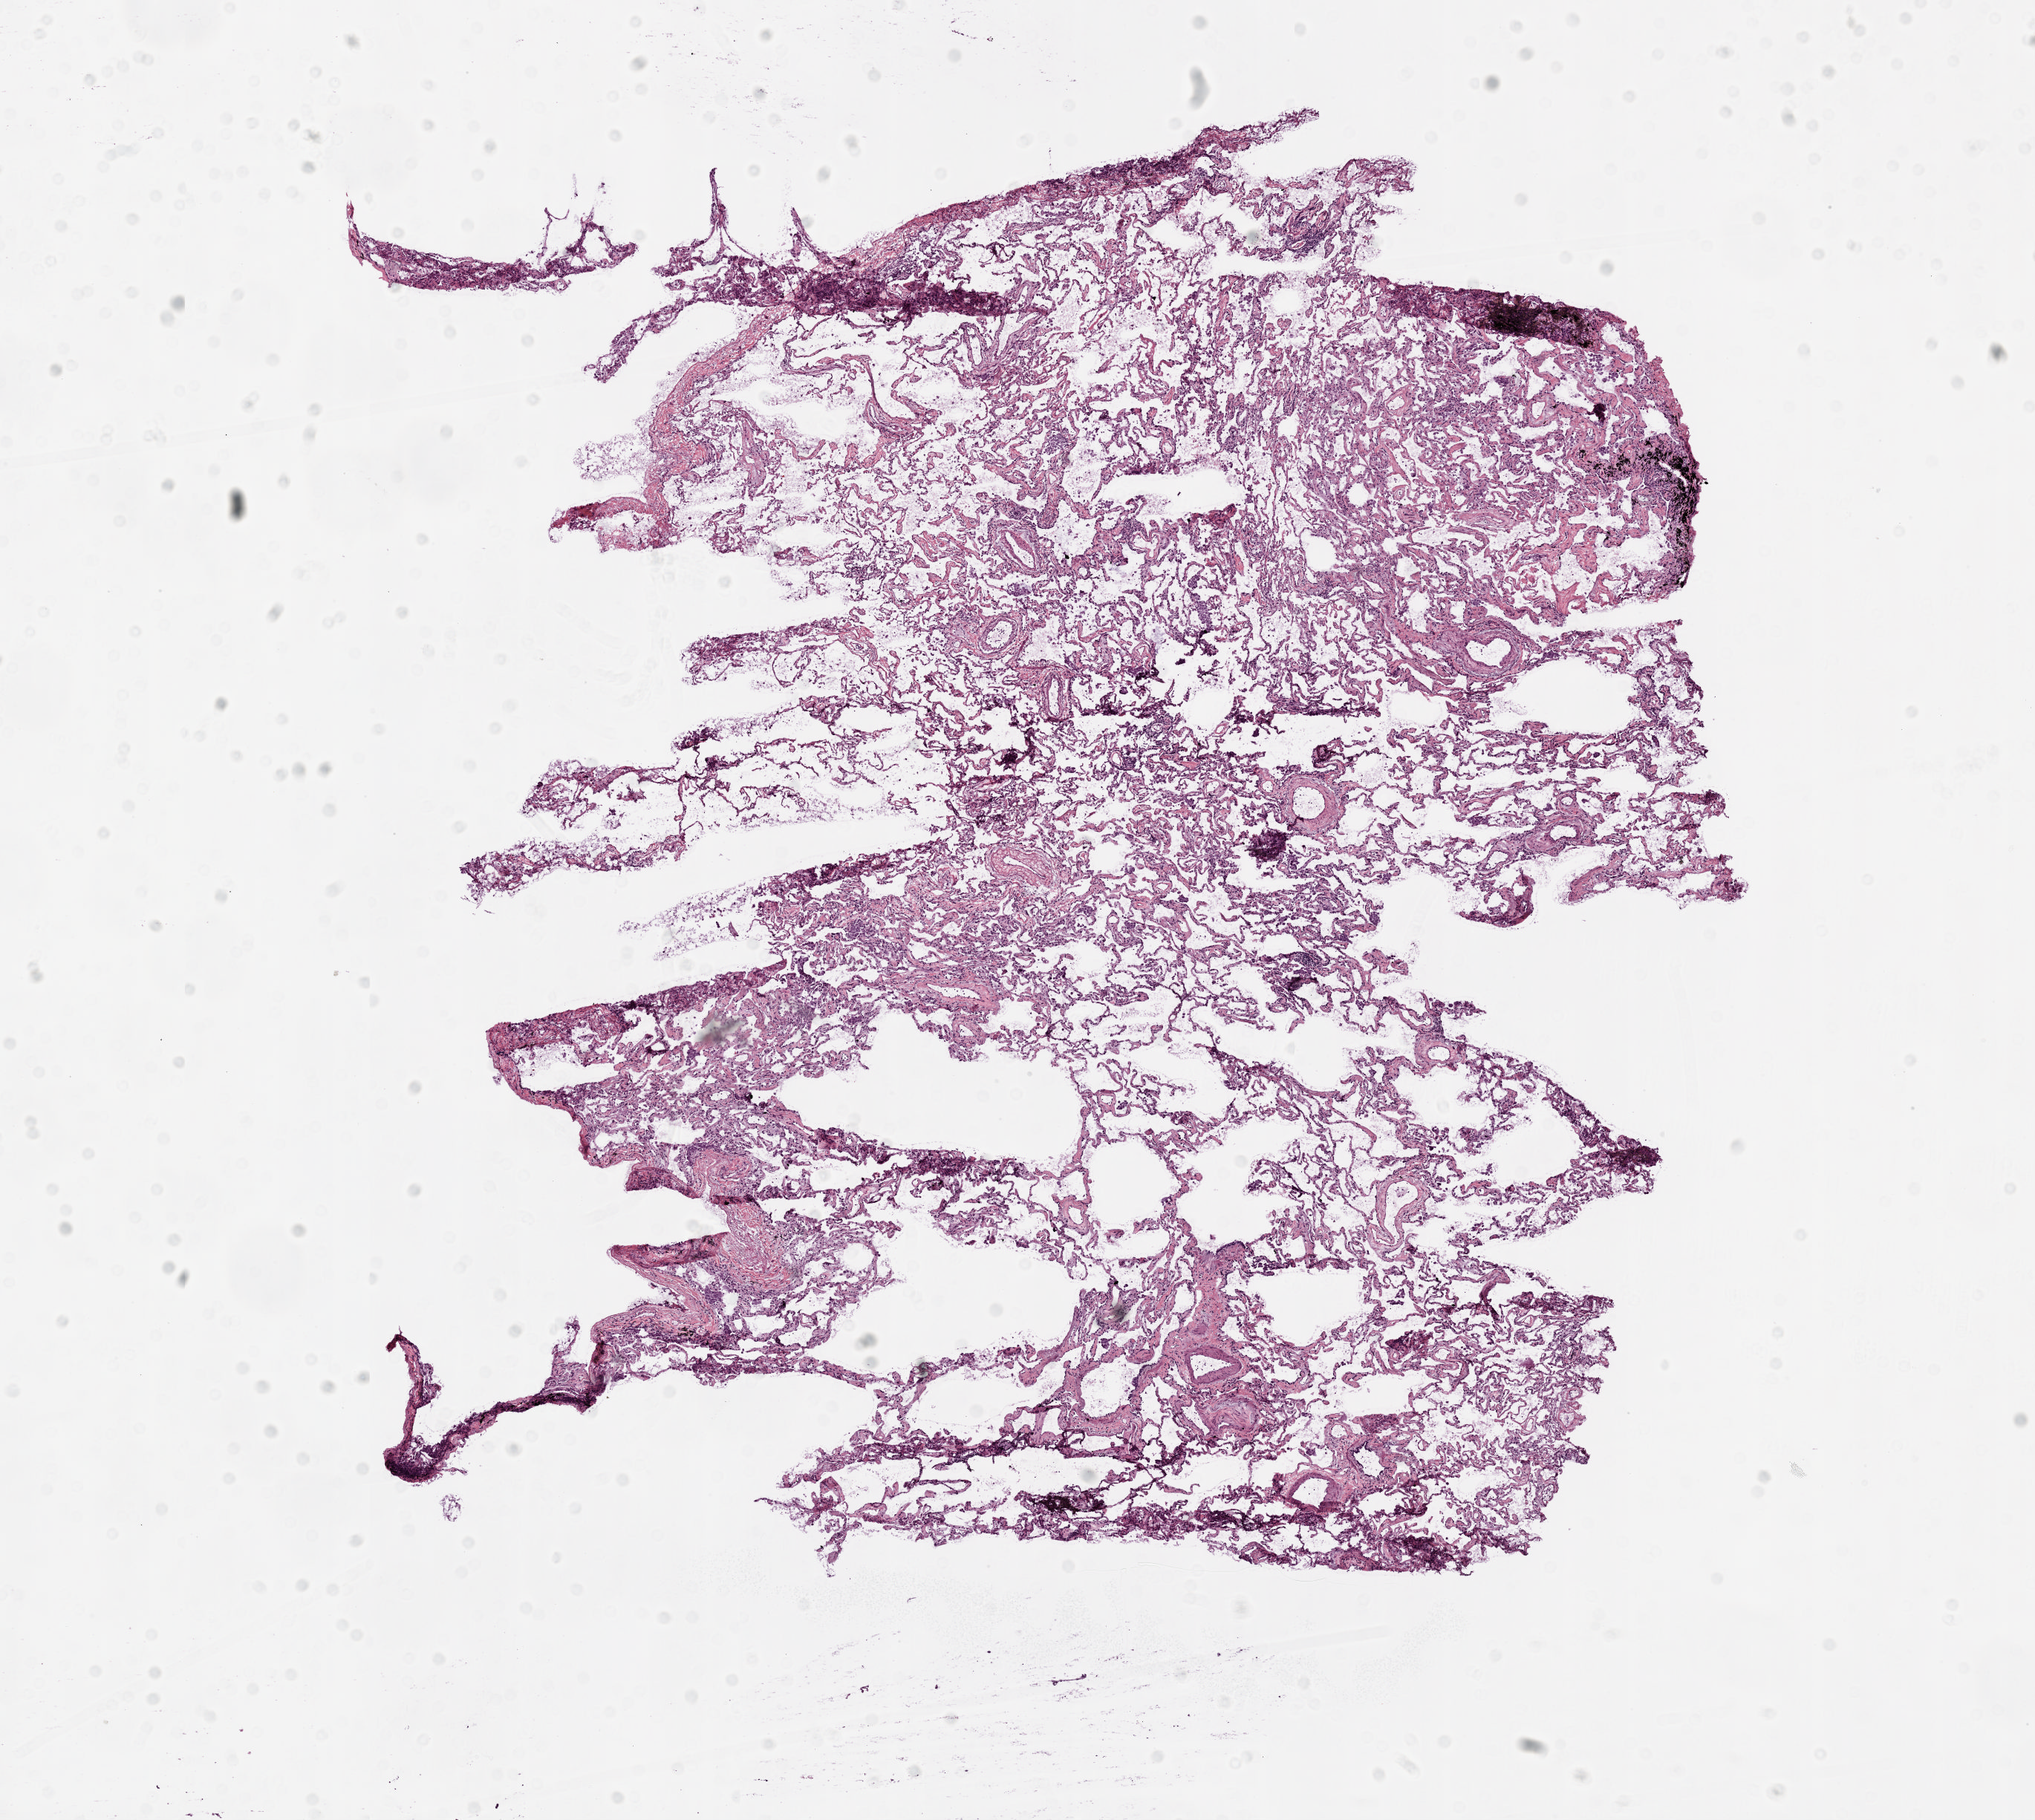
Hematoxylin and eosin (H&E) stained whole-slide image, whole scanned area (about 11.0 x 9.9 mm, acquisition: 20x scan) shown as a low-resolution overview. Frozen section from the top of the tissue portion. Solid tissue normal (non-tumour tissue) sample from the lung. Female, age 83 years at initial diagnosis.
* this section: solid tissue normal sample (biorepository sample class)
* patient diagnosis: Squamous cell carcinoma, NOS